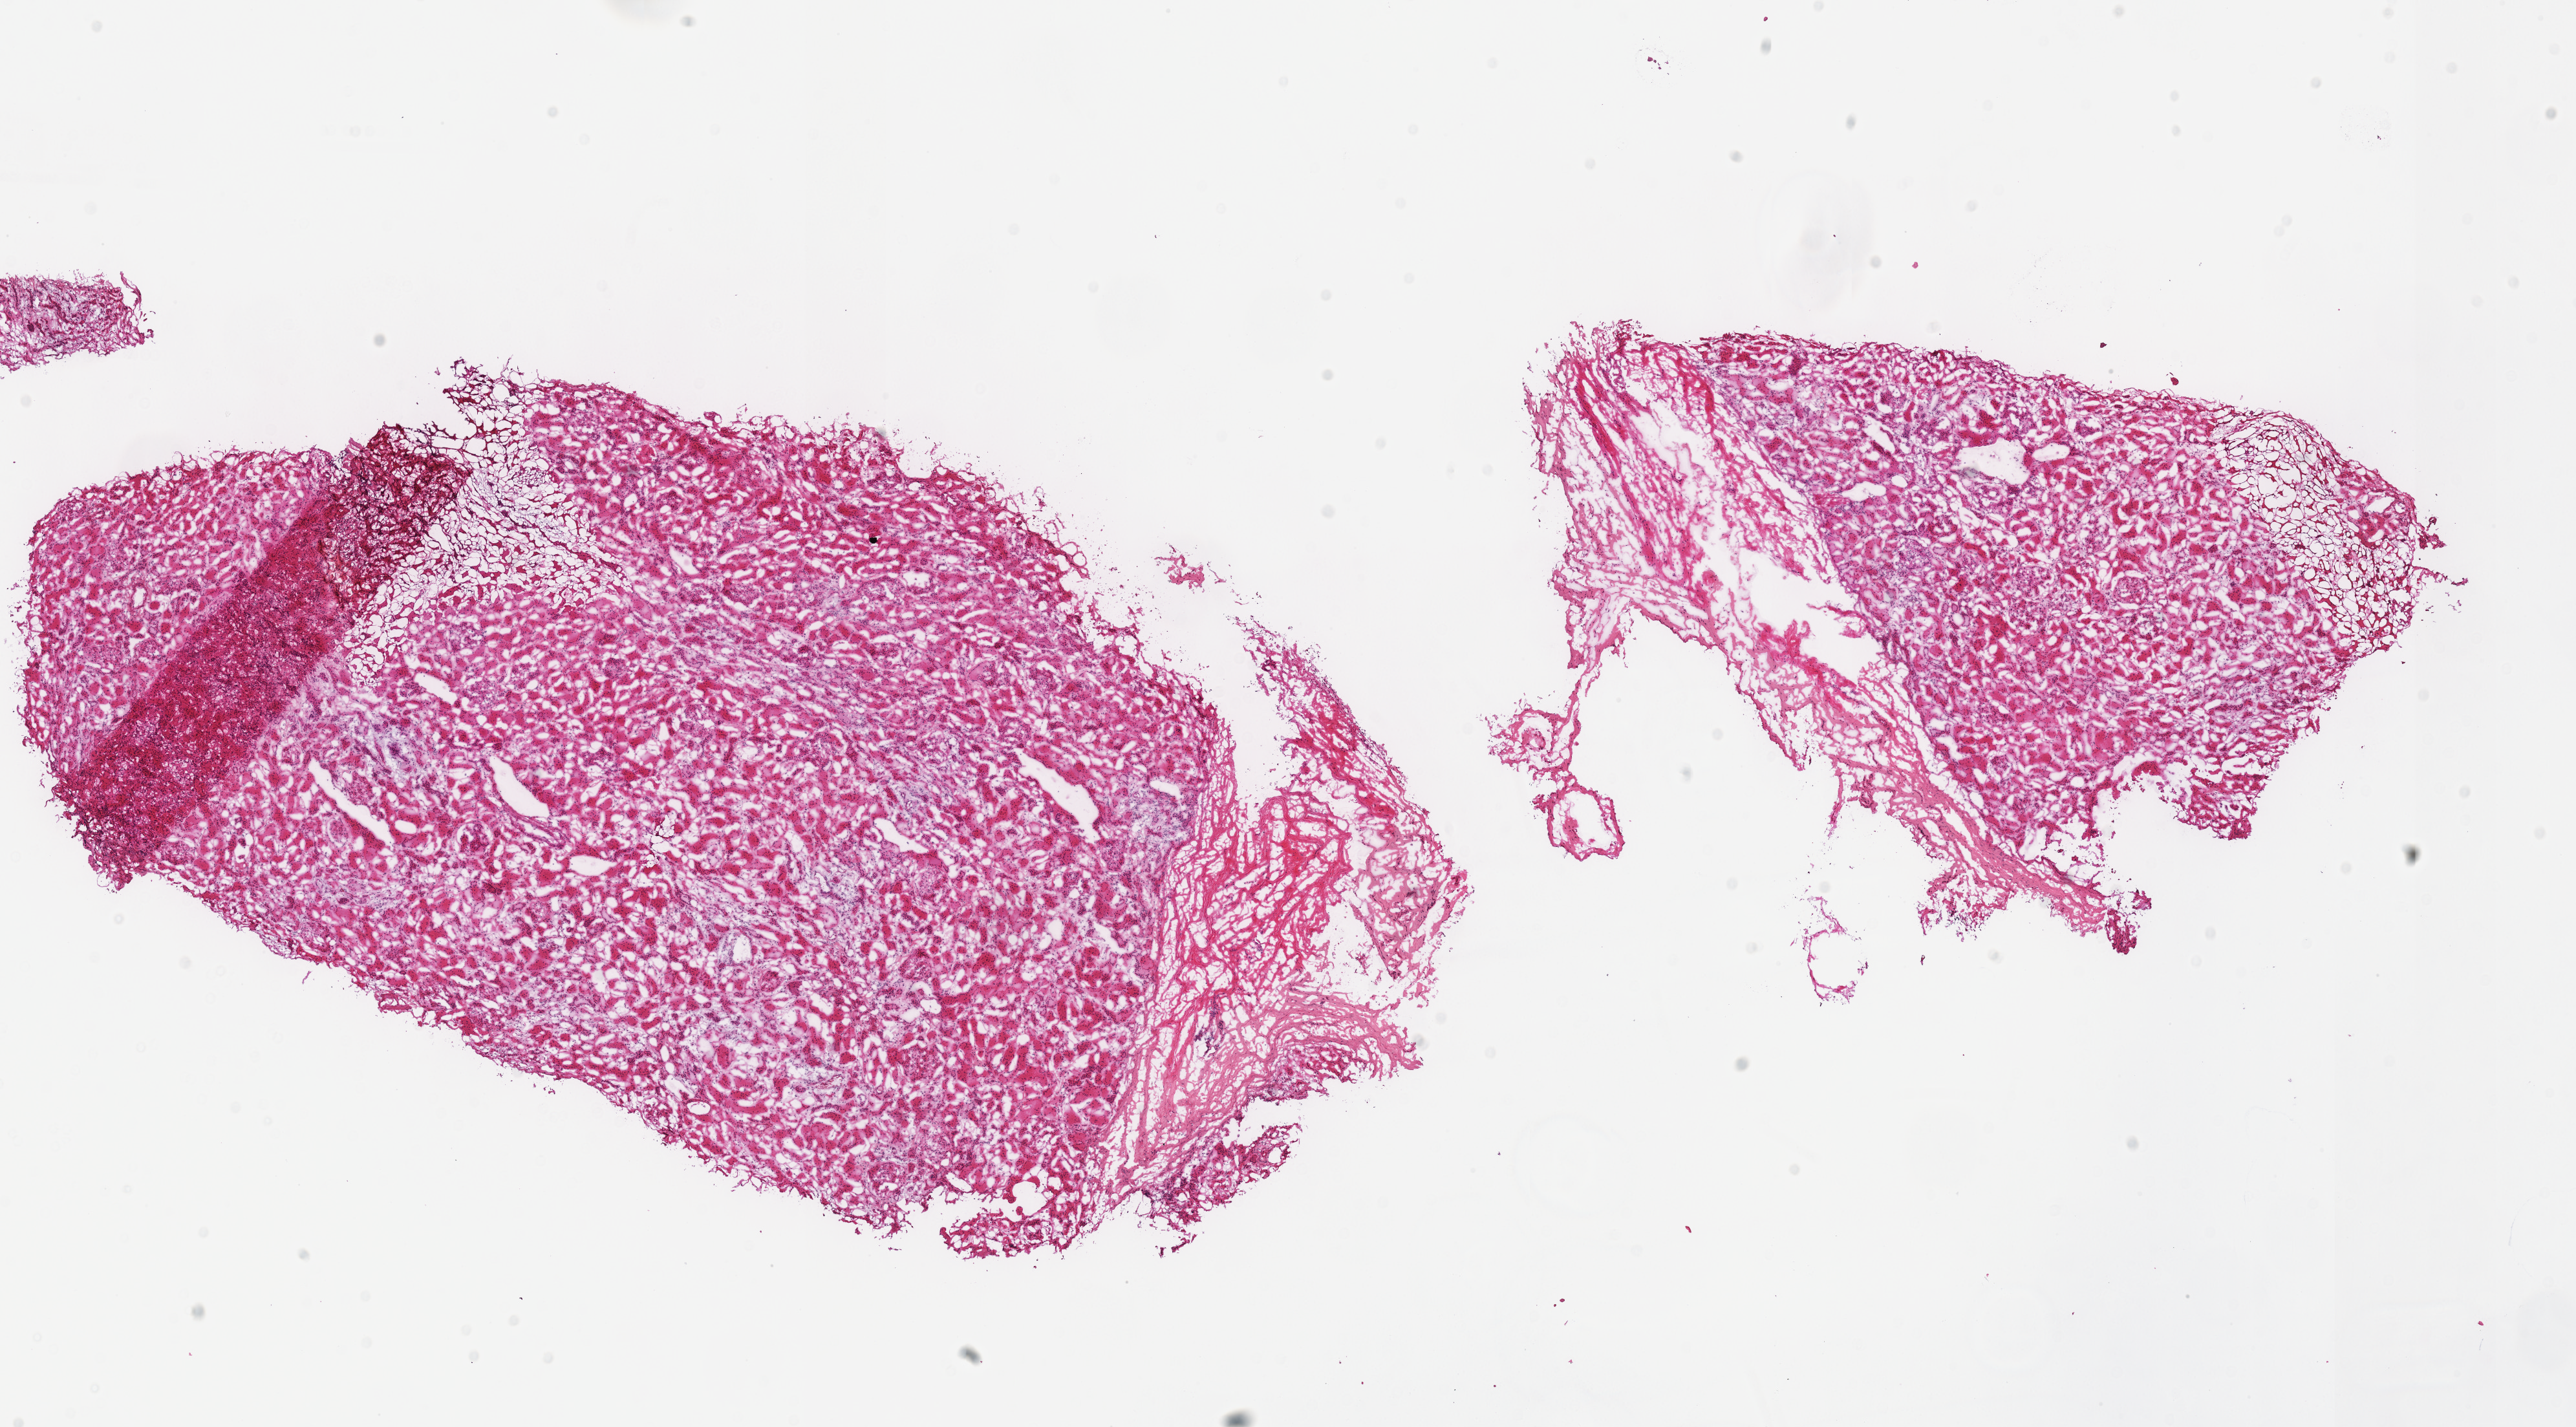
Whole-slide histology image, H&E — low-resolution overview of the scanned area, about 15.7 x 8.7 mm. Frozen section from the top of the tissue portion. Sample: solid tissue normal (non-tumour tissue), kidney. Female patient; age at initial diagnosis 50 years.
- this section: solid tissue normal (non-tumour) sample from the same patient
- patient diagnosis: Renal cell carcinoma, chromophobe type